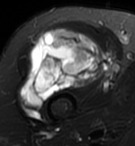
MRI of an extremity soft-tissue mass, one axial slice; slice 69 of 95 in the series (ordered by position); T2-weighted fat-saturated; MR volume resampled by the dataset authors to the PET/CT grid (not the native acquisition matrix); 3.27 mm slice thickness; 135 × 146 image matrix, field of view 132 × 143 mm. Female patient. Case-level facts recorded for this patient, not image findings: histological type: pleiomorphic undifferentiated sarcoma; grade: high; site of the primary tumour: right quadricep.
Structures marked on this image (expert contour drawn on MRI and transferred to this co-registered scan by the dataset authors):
- gross tumour volume including surrounding oedema: bounding box (x1, y1, x2, y2) in pixels: (21, 27, 102, 108)
- gross tumour volume (mass): (21, 27, 102, 108)